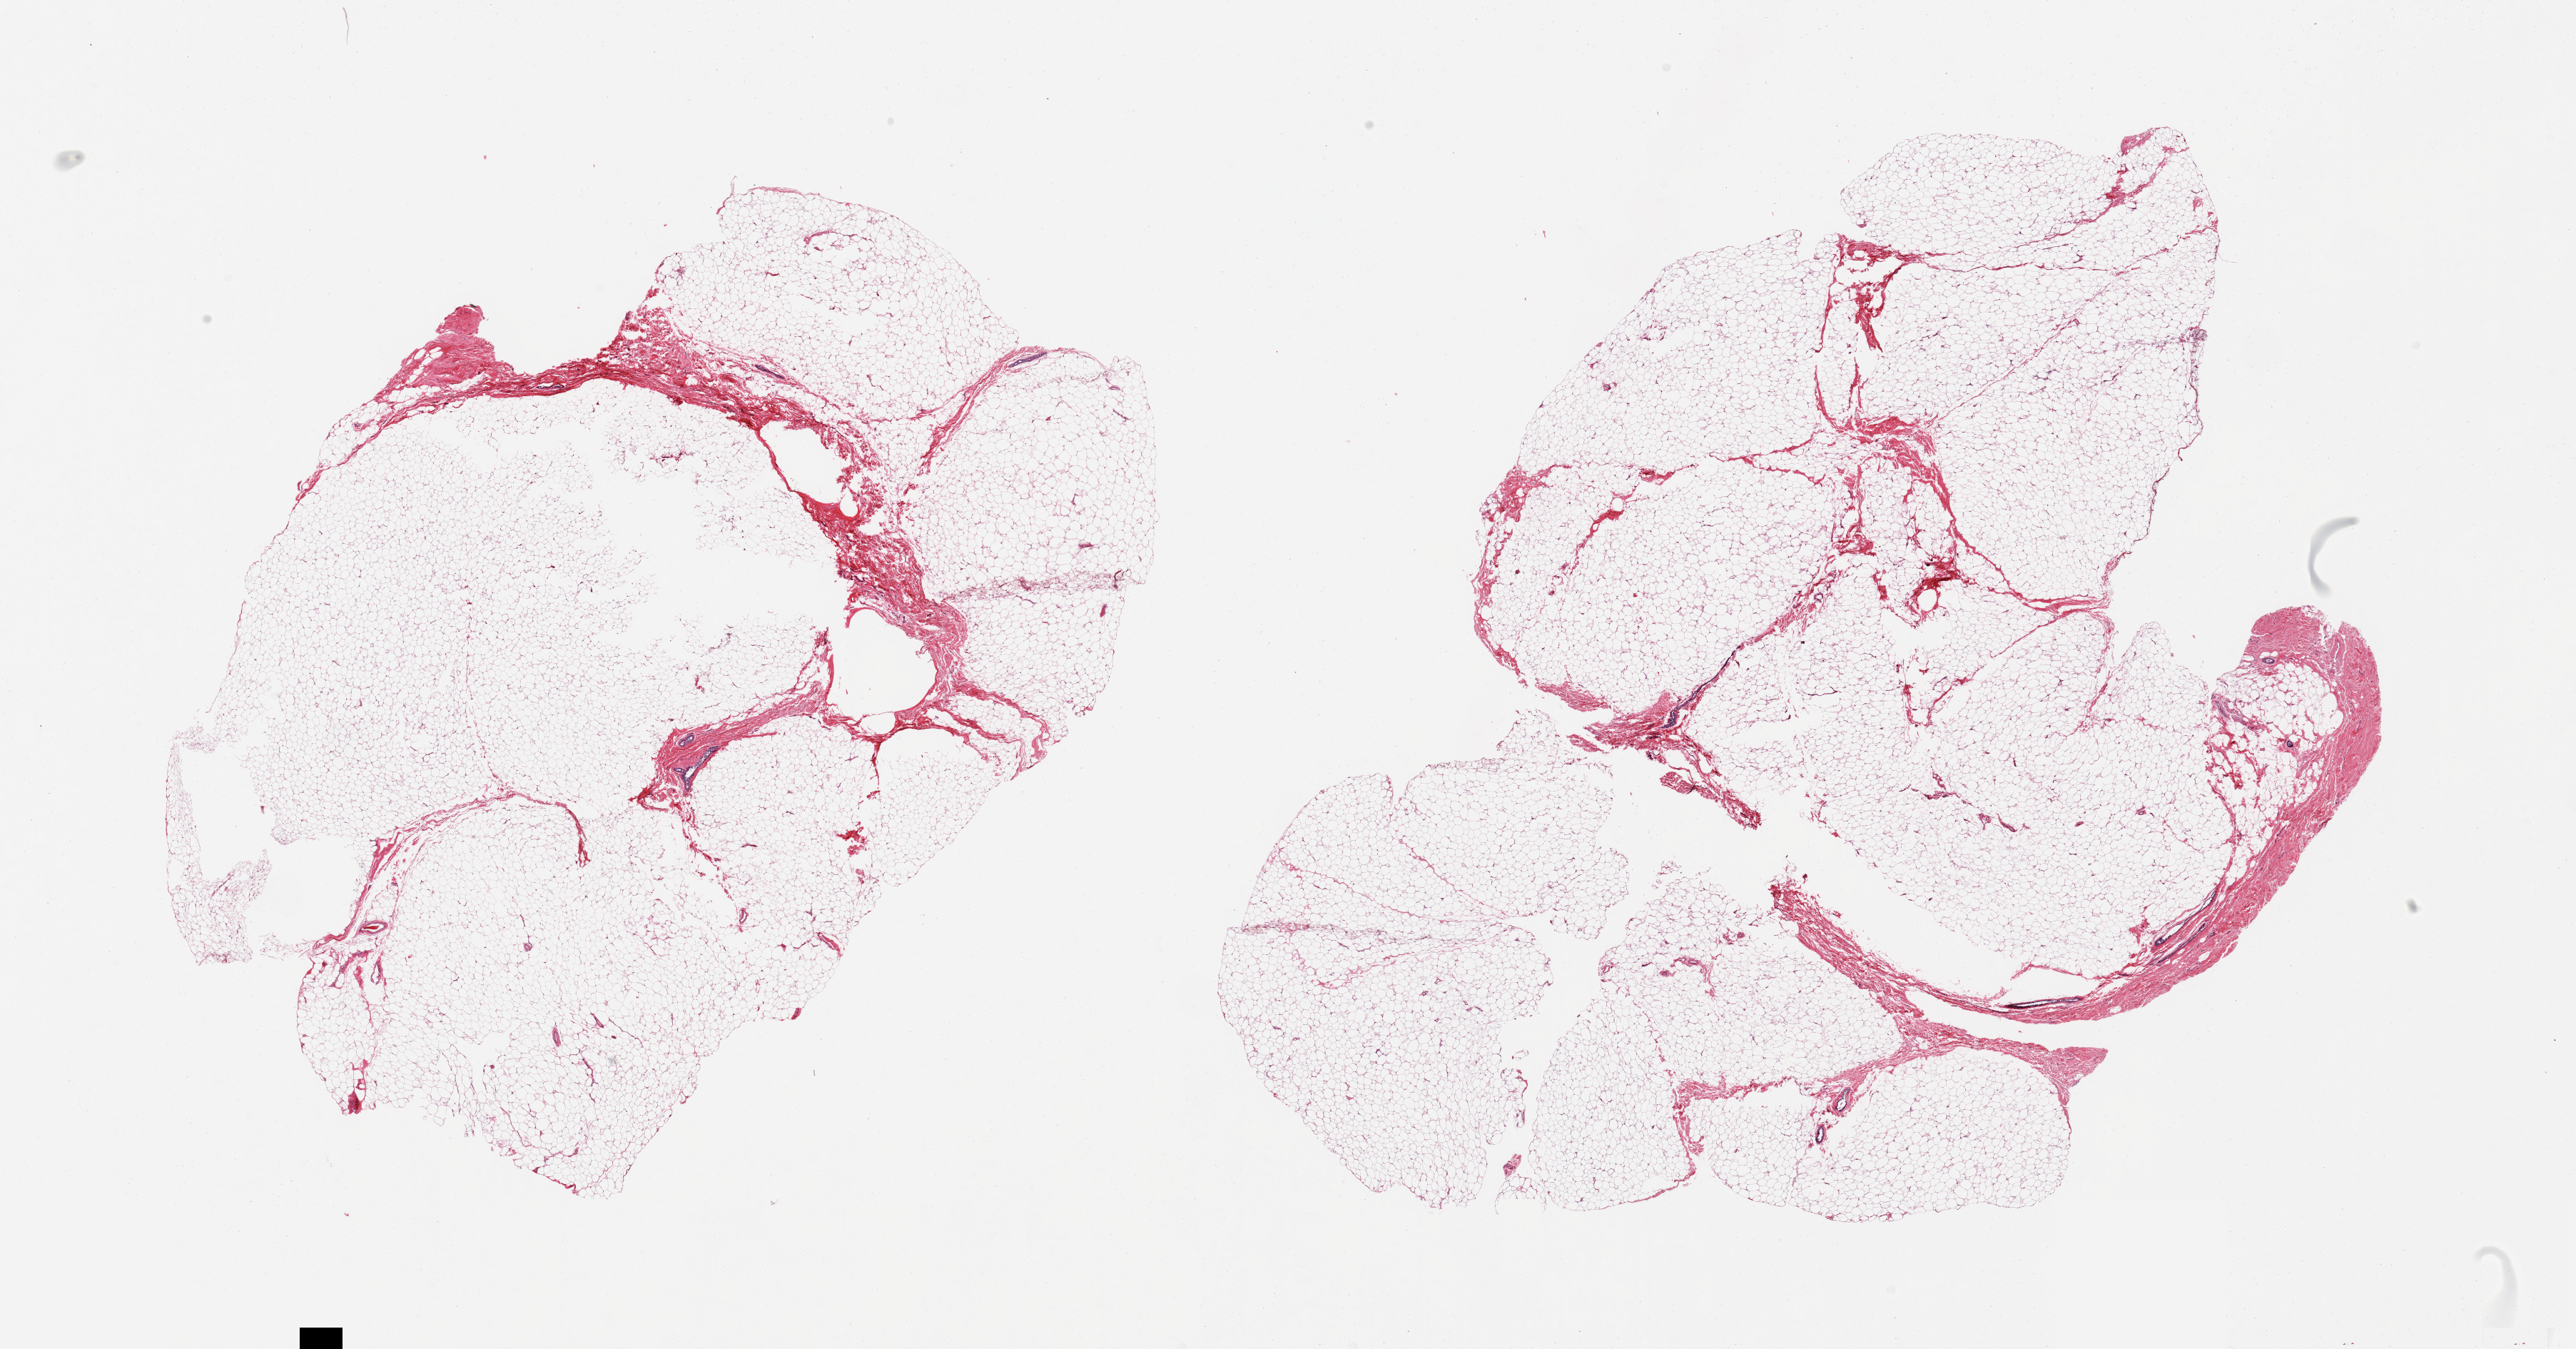
Whole-slide image, haematoxylin and eosin stain, low-resolution overview of the scanned area, about 28.5 x 14.9 mm, PAXgene-fixed paraffin-embedded (PFPE) section, section of breast (target tissue), donor tissue sample.
* reviewer comment on this tissue sample: 2 pieces, mainly fibroadipose elements; Trace ductal elements